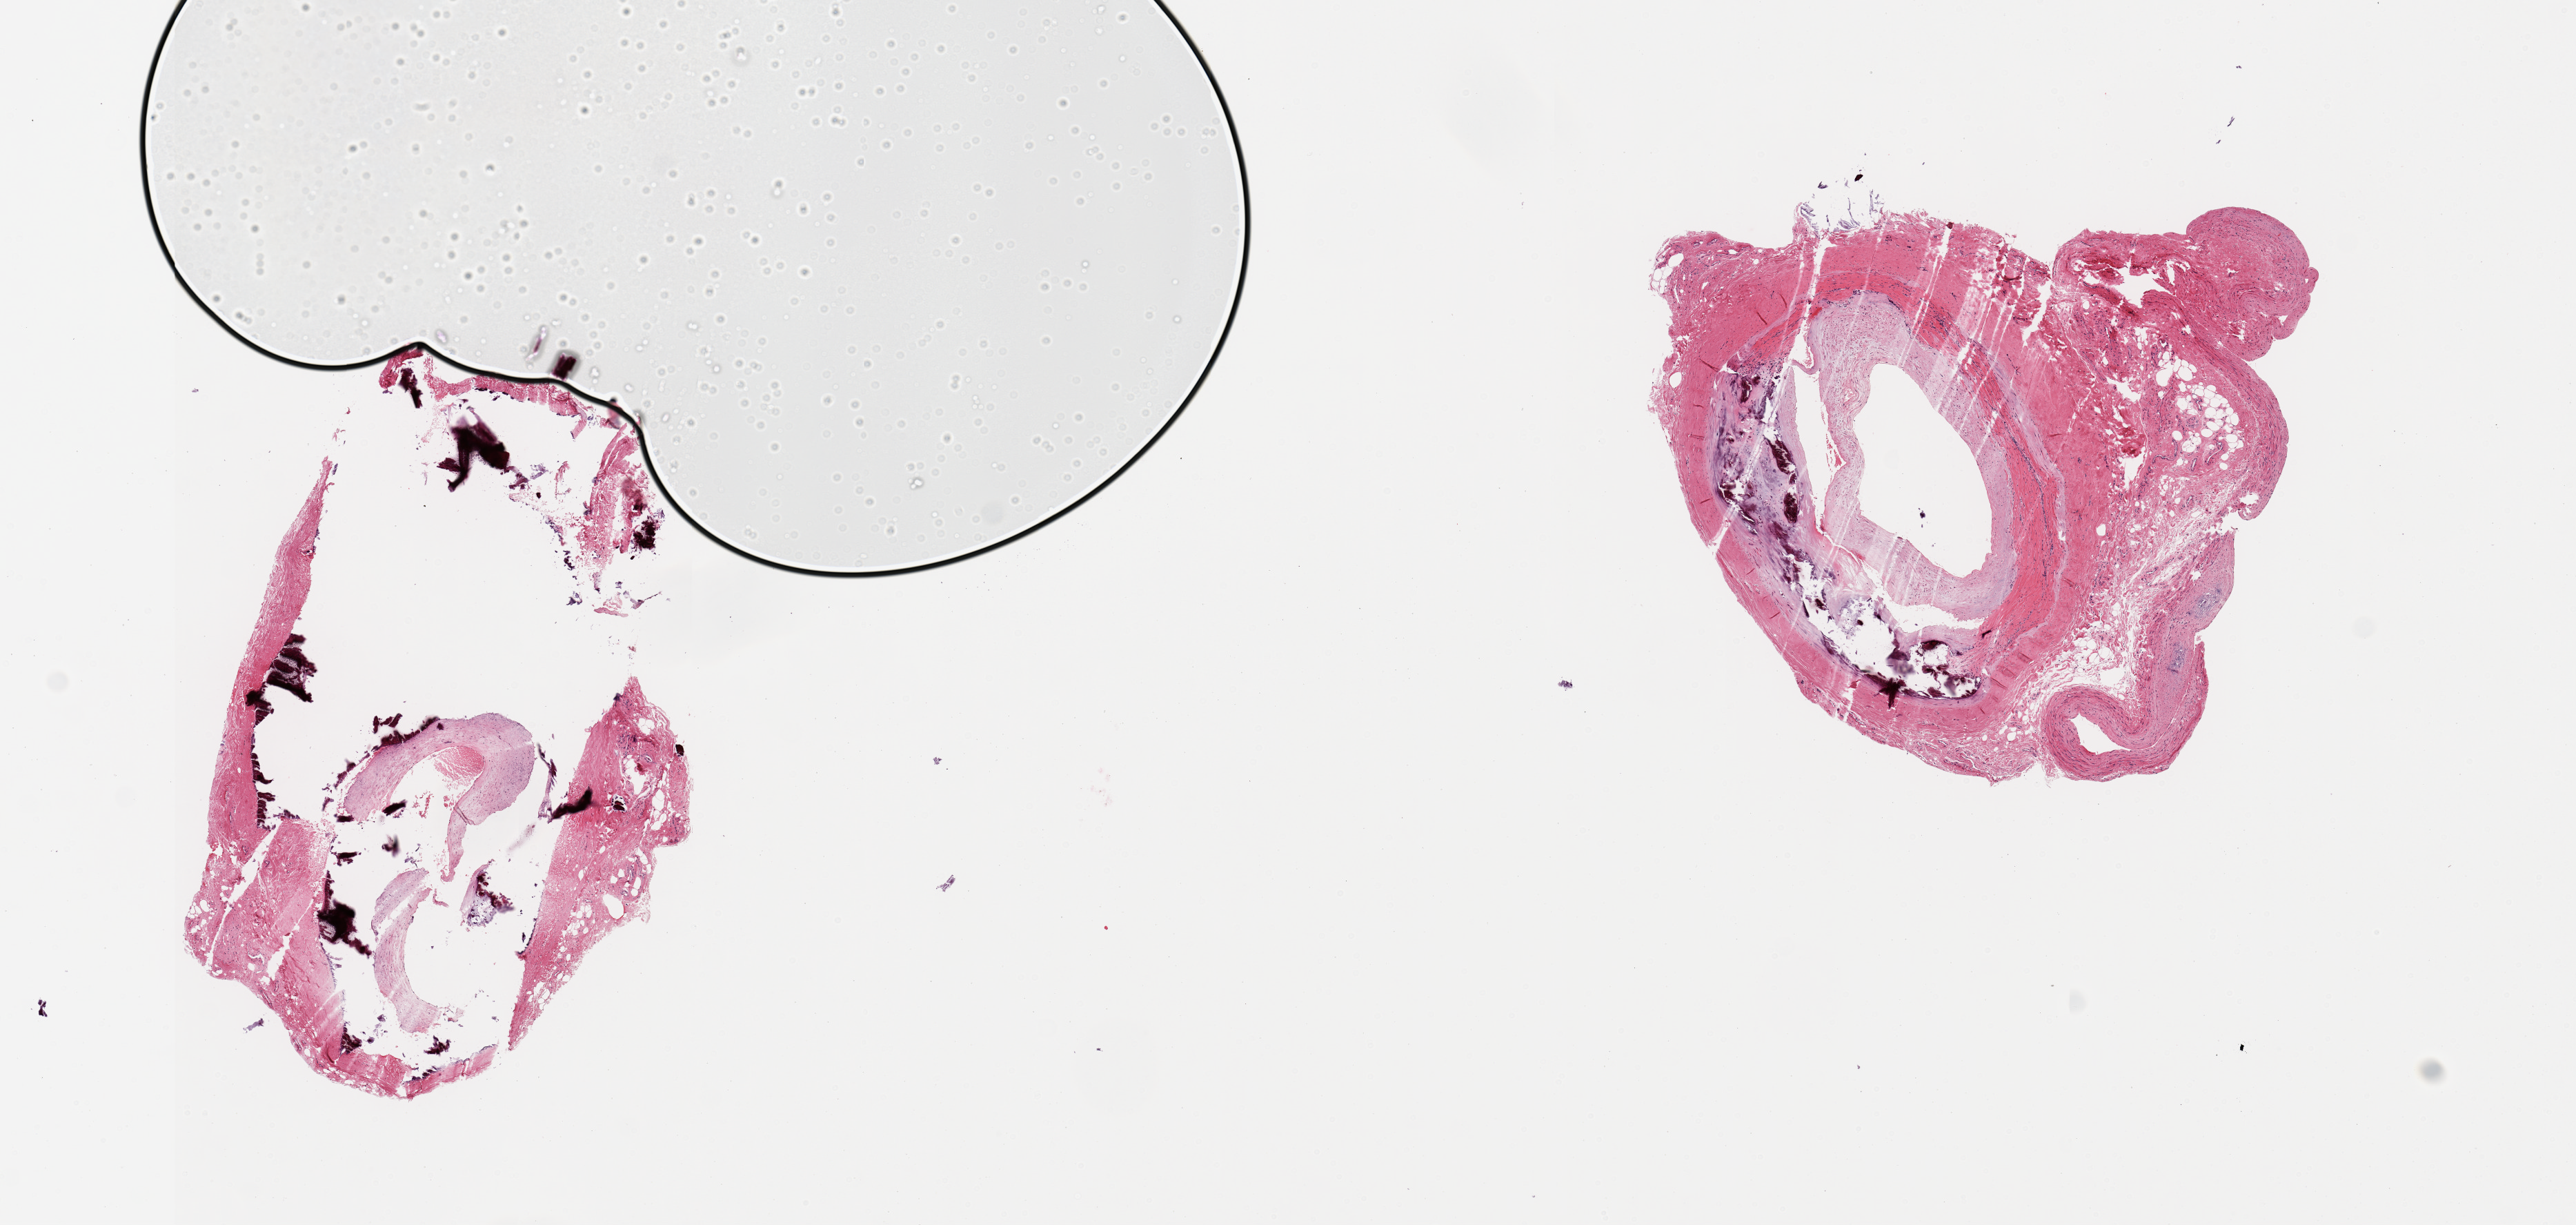
Haematoxylin and eosin whole-slide image — a low-resolution overview of the entire scanned area, about 14.8 x 7.0 mm. PAXgene-fixed paraffin-embedded (PFPE) section. Section of tibial artery (target tissue). Tissue donor sample. Donor: male.
* review note (as recorded): 2 pieces; one is fragmented due to calcification, atherosclerosis with narrowing of the lumen by >50%